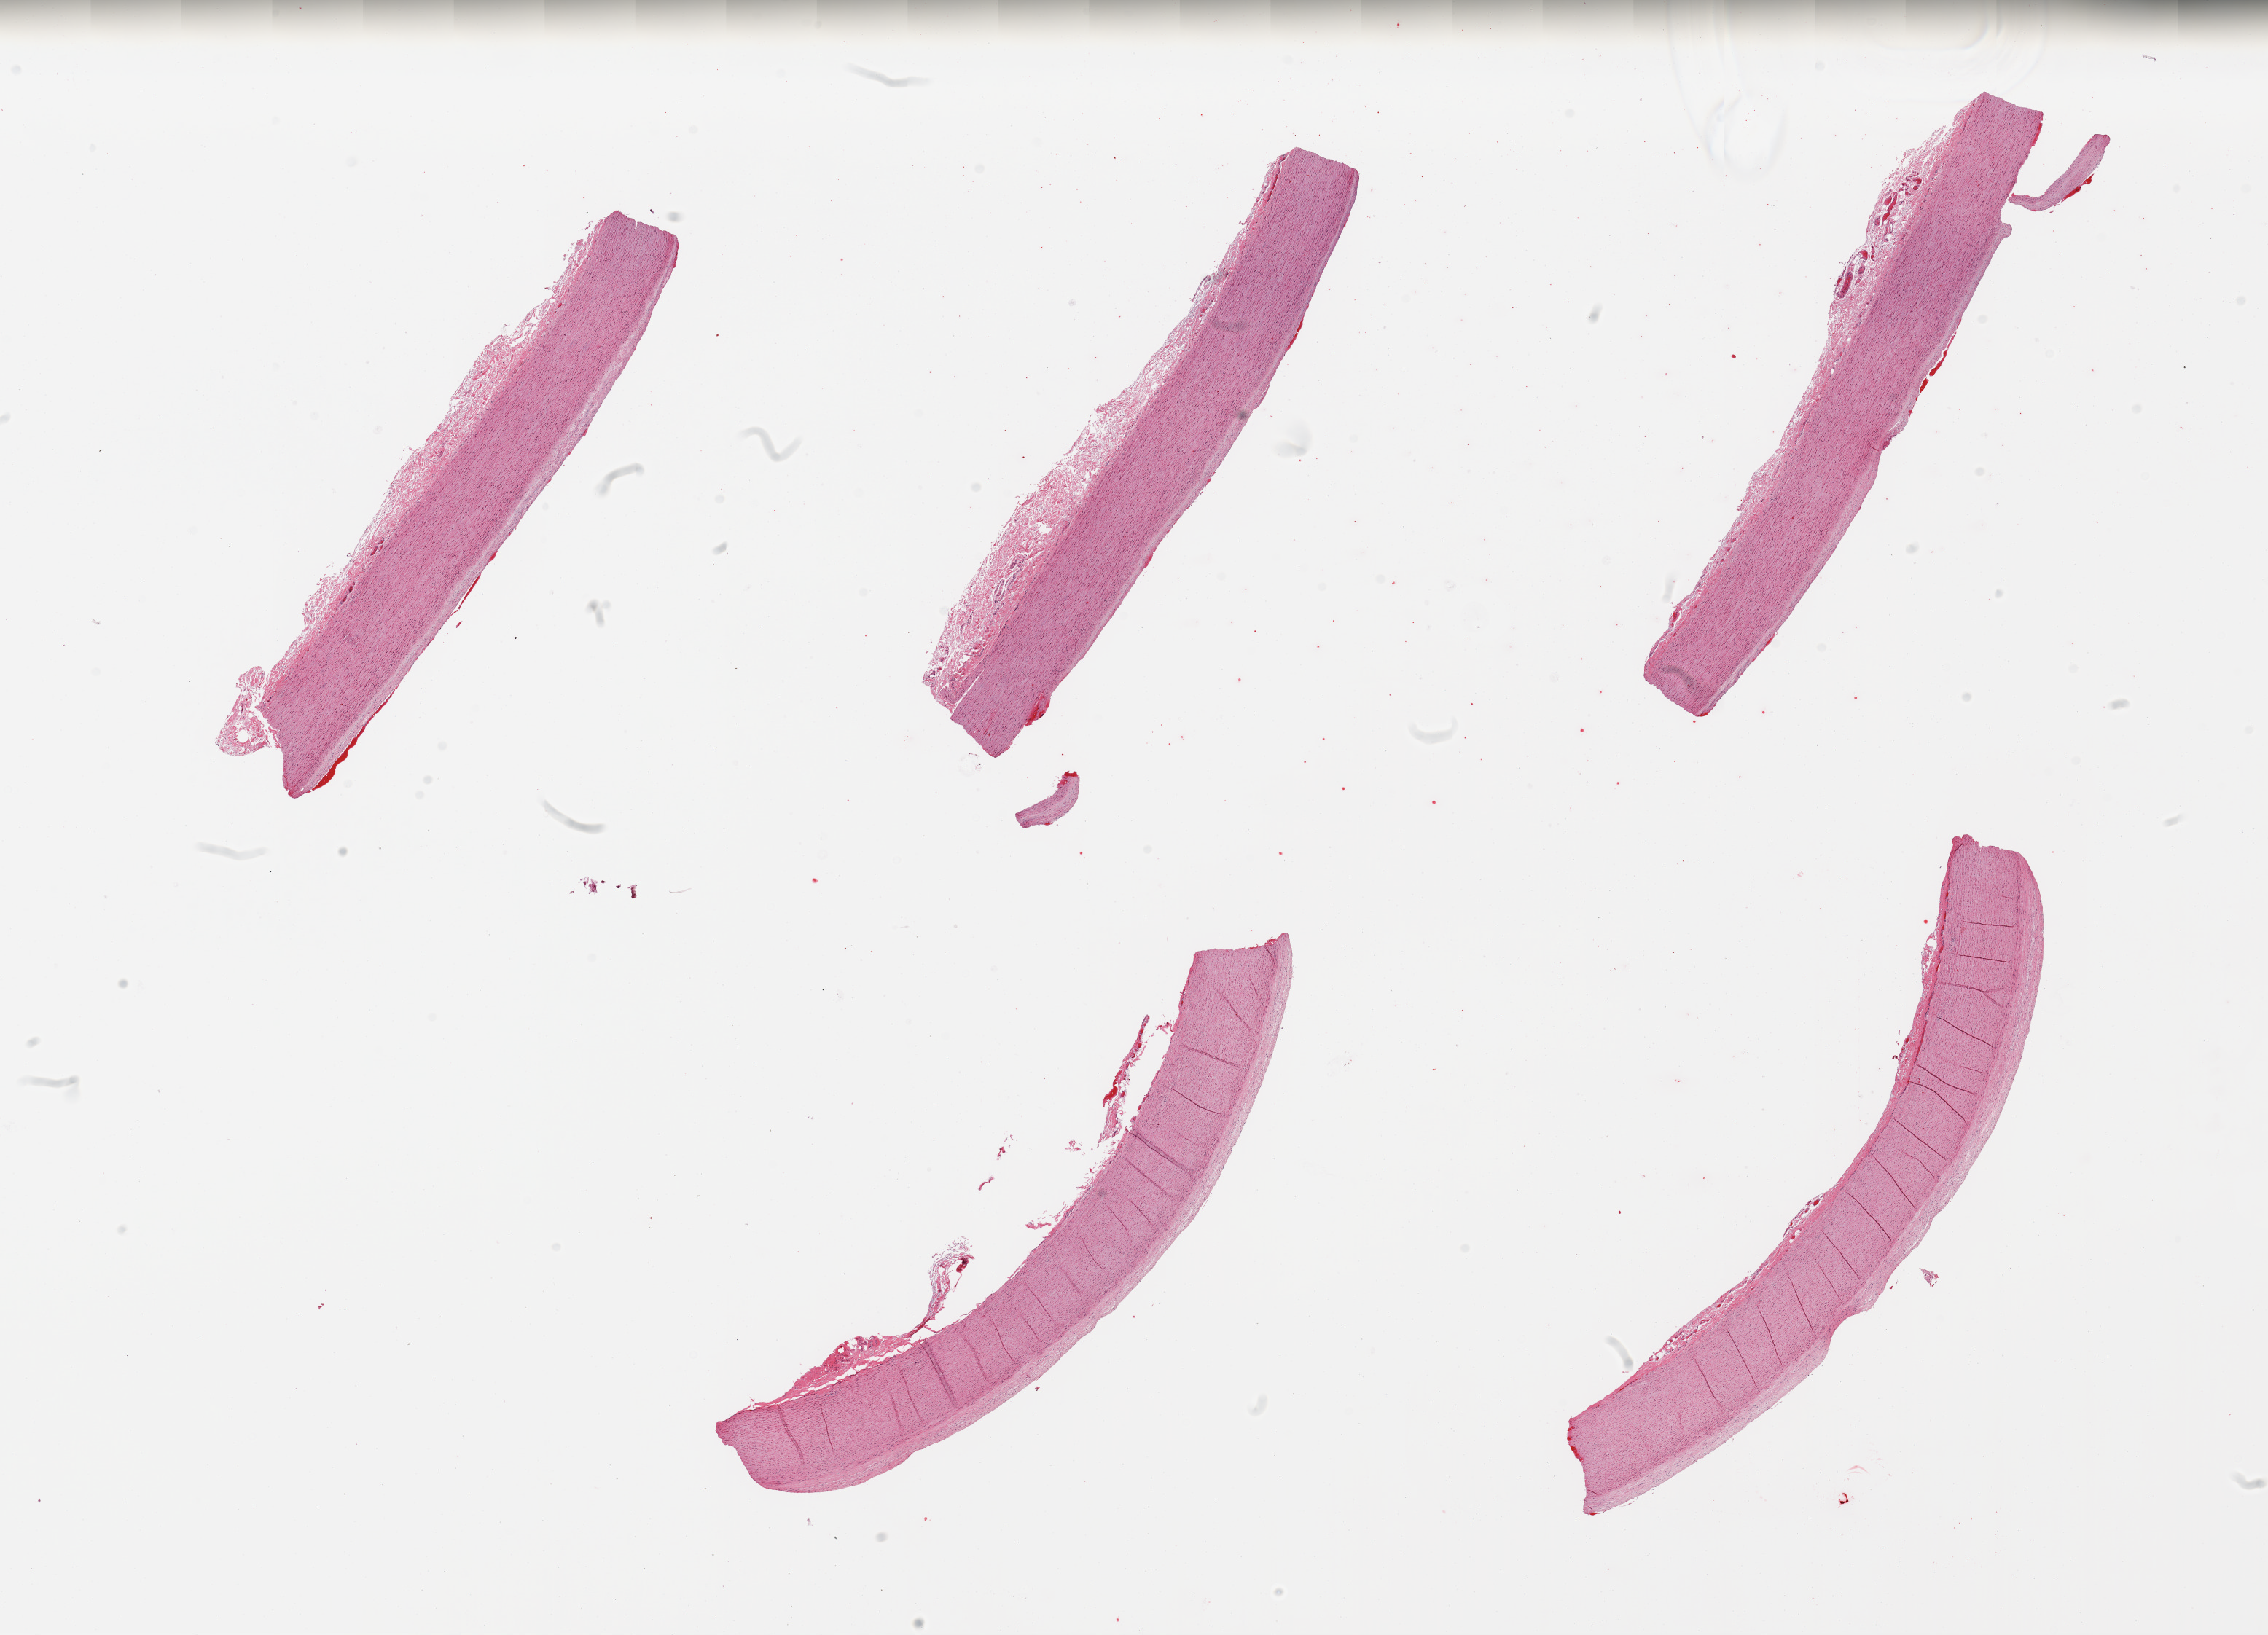
Haematoxylin and eosin whole-slide image — low-resolution overview of the scanned area, about 24.6 x 17.7 mm; PAXgene-fixed paraffin-embedded (PFPE) section; target tissue: aorta; tissue donor sample. Donor sex: female.
Reviewer comment on this tissue sample: 6 pieces; mild atheromatous change.